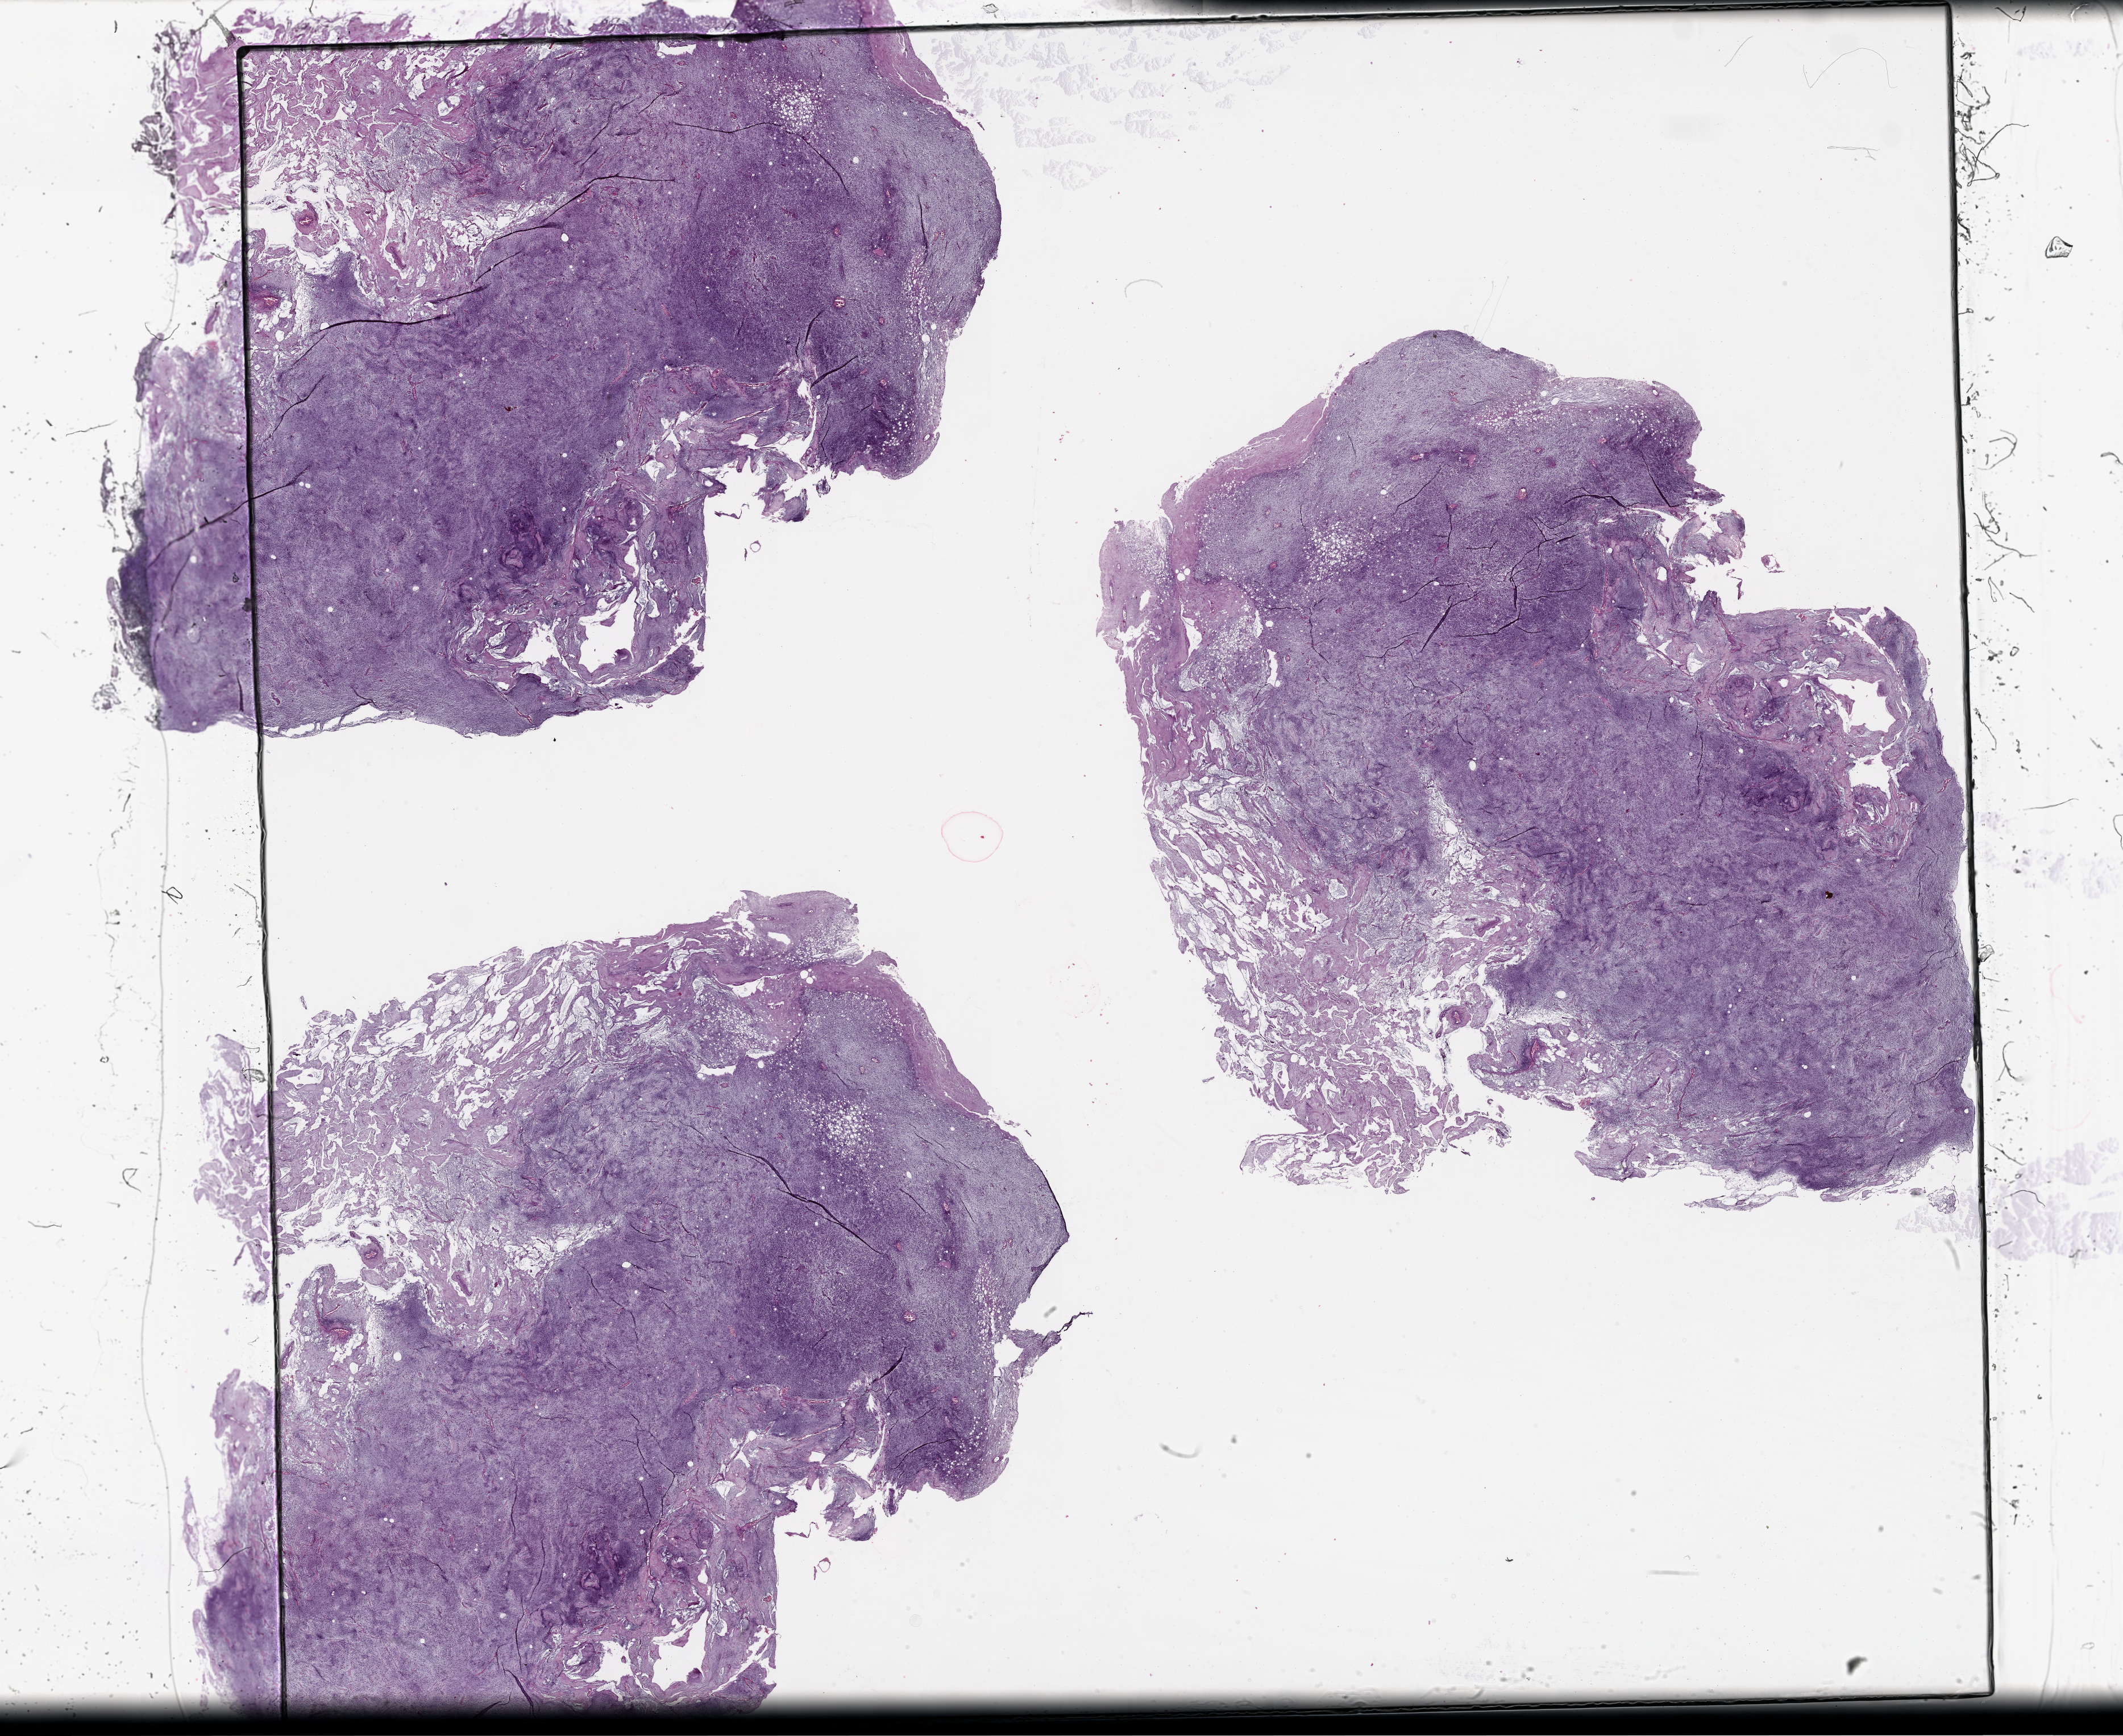
H&E whole-slide image — whole scanned area (about 30.1 x 24.6 mm, from a 20x scan) shown as a low-resolution overview, tumour tissue sample. Female, 78 y/o.
* primary tumour site (as recorded): lower extremity
* patient diagnosis (cohort enrolment): sarcoma (site not recorded at cohort level)